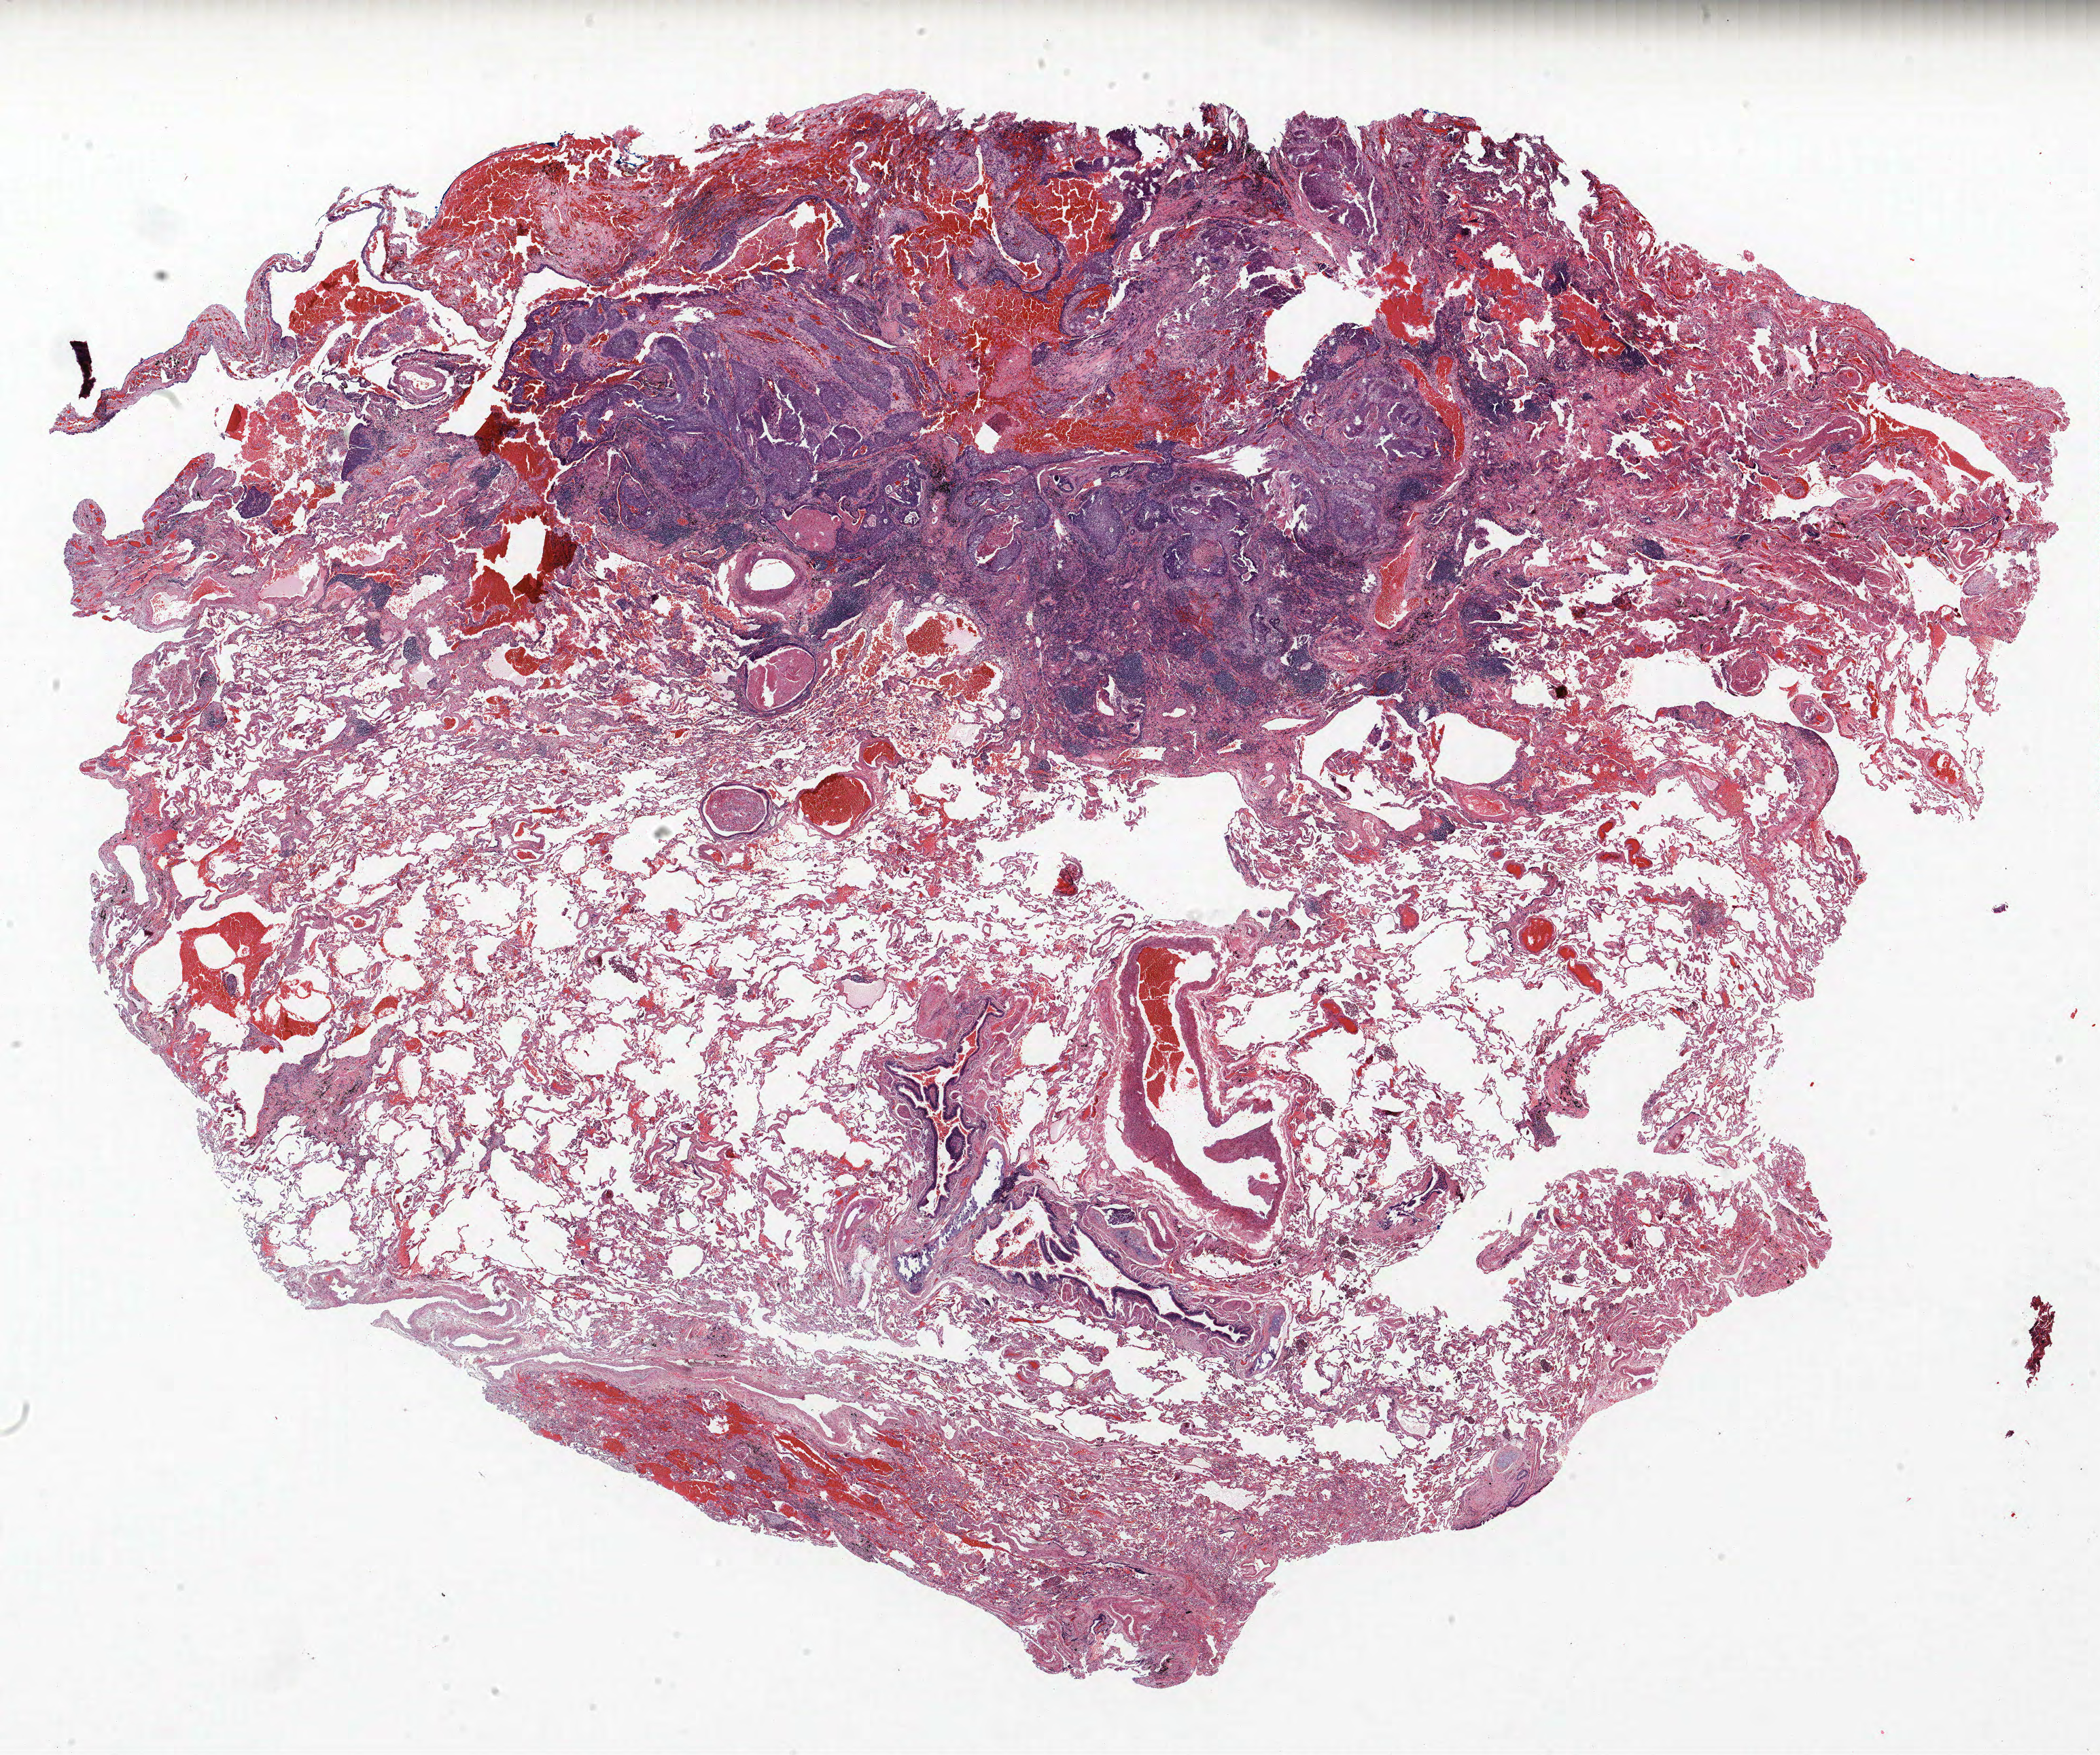
Whole-slide histology image, Hematoxylin and eosin (H&E) stained, a low-resolution overview of the entire scanned area, about 24.7 x 20.7 mm. Formalin-fixed paraffin-embedded (FFPE) section. Lung. Male patient, aged 65 at enrolment. Former smoker at enrolment.
Tumour size (pathology): 20 mm. Stage (AJCC 6th edition): IB. Participant's lung-cancer diagnosis: Squamous cell carcinoma, NOS. Primary tumour location (clinical record): left upper lobe.